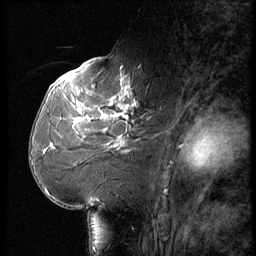
Breast MRI (dynamic contrast-enhanced), one sagittal slice. Position 32 of 56 along the scan axis. Dynamic contrast-enhanced series, image 2 of 3 at this slice position (ordered by acquisition). 1.5 T. TE 4.2 ms, TR 9 ms. 256 × 256 image matrix, field of view 180 × 180 mm. Patient: female, 61 years. Case-level facts recorded for this patient, not image findings: setting: breast cancer imaged before/during neoadjuvant chemotherapy; receptor status: HR-positive, HER2-negative.
Outlined on this slice (semi-automatically segmented with operator editing):
- analysis volume of interest (the breast-tissue region the enhancement analysis was run in; not a lesion): bounding box [x1, y1, x2, y2] px = [65, 74, 156, 175]
- tumour enhancement mask (voxels above the 140 % enhancement threshold inside the analysis volume of interest): [74, 77, 136, 143]